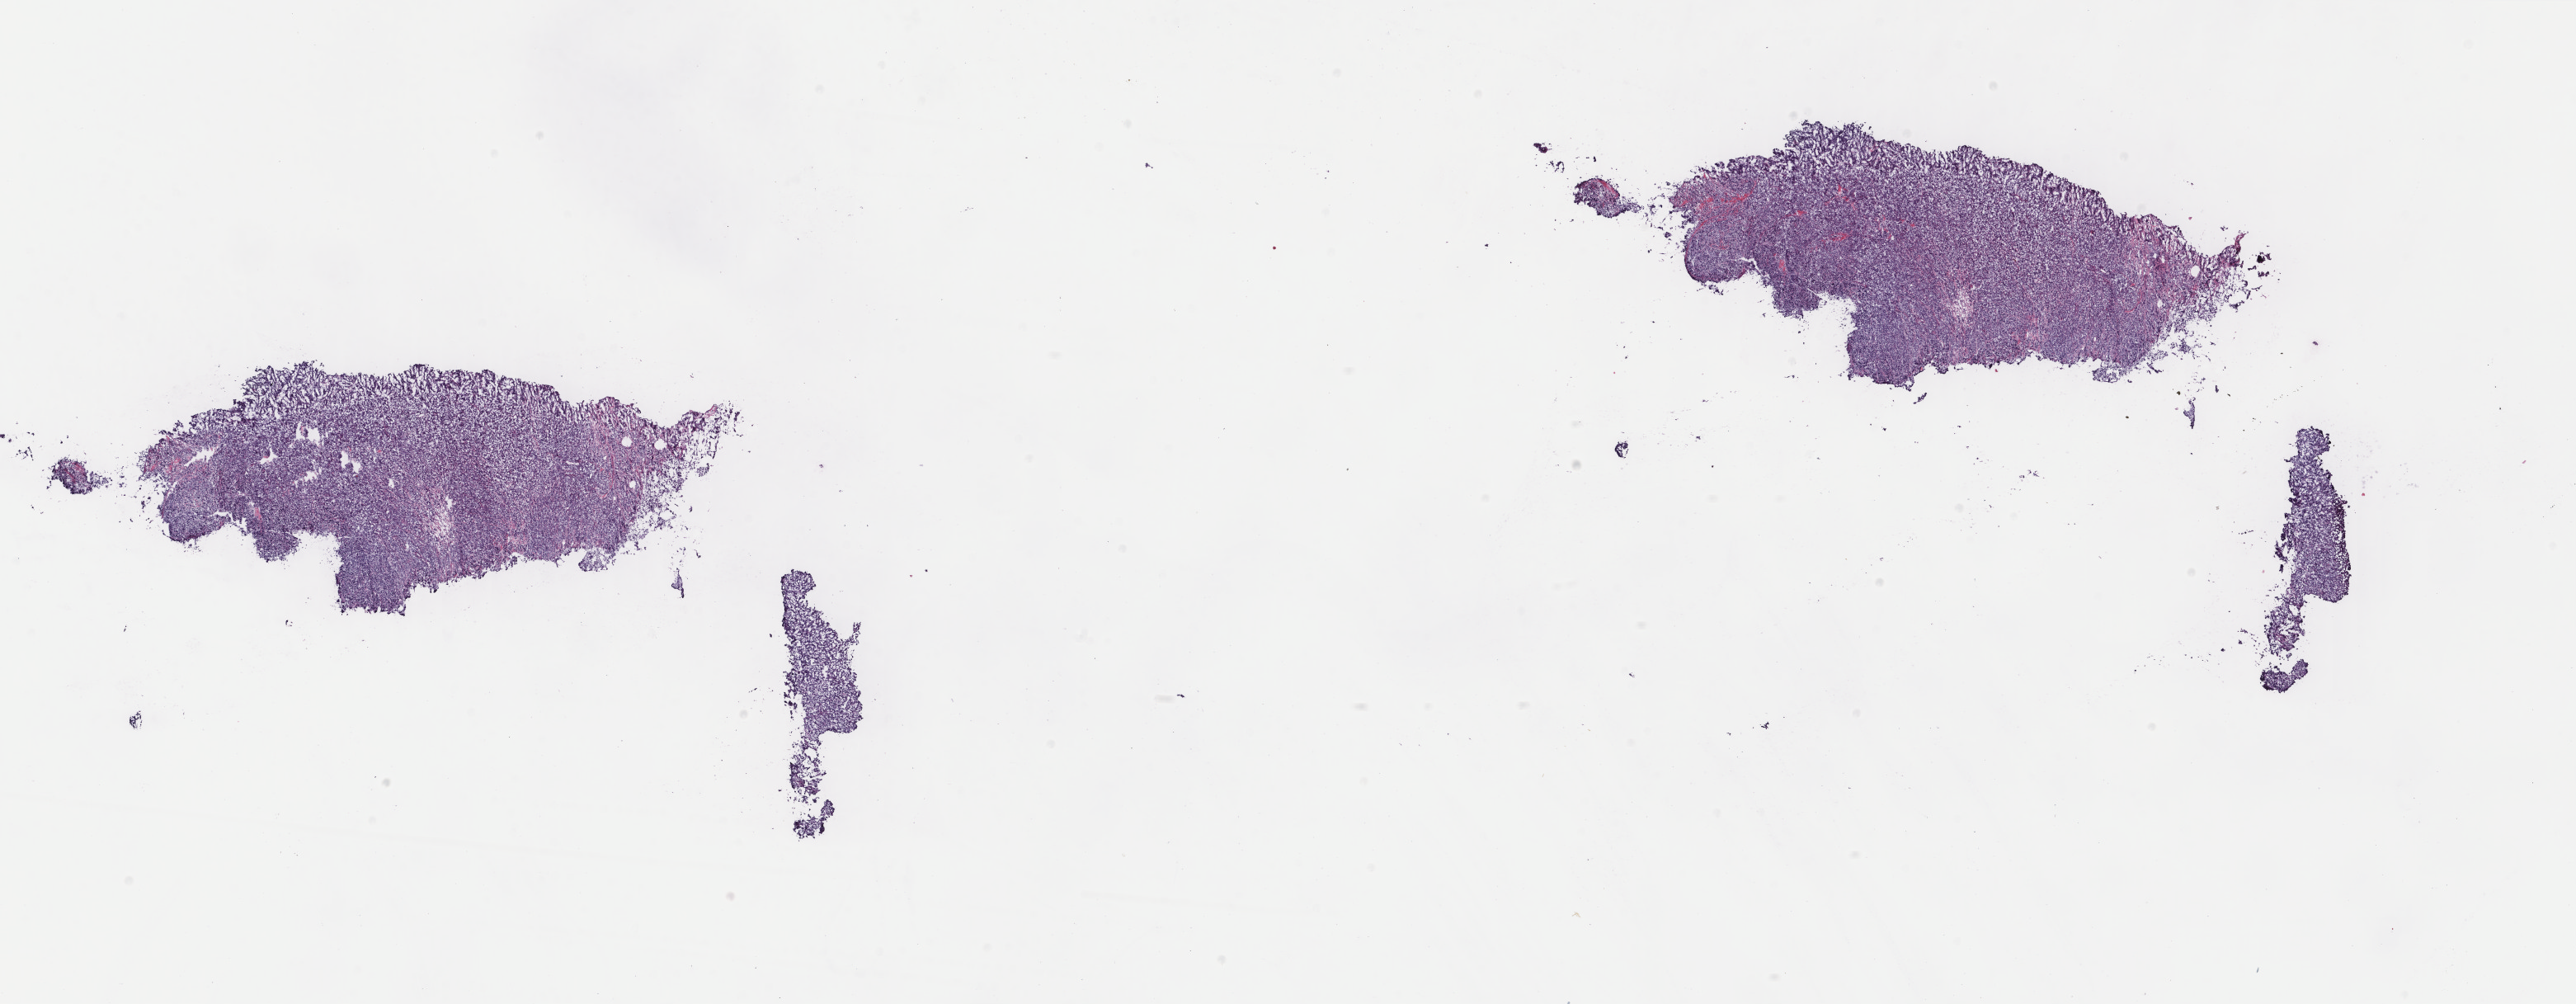
H&E-stained whole-slide image, shown as a low-resolution overview of the whole scanned area (about 24.8 x 9.7 mm), frozen section from the bottom of the tissue portion, breast, primary tumour sample. Patient: female, age at initial diagnosis 61 years. Composition of this section per pathologist review: tumour cells 82%, tumour nuclei 90%, normal cells 0%, stromal cells 8%, necrosis 10%. Inflammatory infiltration, as recorded: lymphocyte infiltration 3%, monocyte infiltration 0%, neutrophil infiltration 0%.
AJCC pathologic stage: IIA. TNM: T2 N0 (i-) M0. Pathologic diagnosis: Infiltrating duct carcinoma, NOS. Laterality: right.